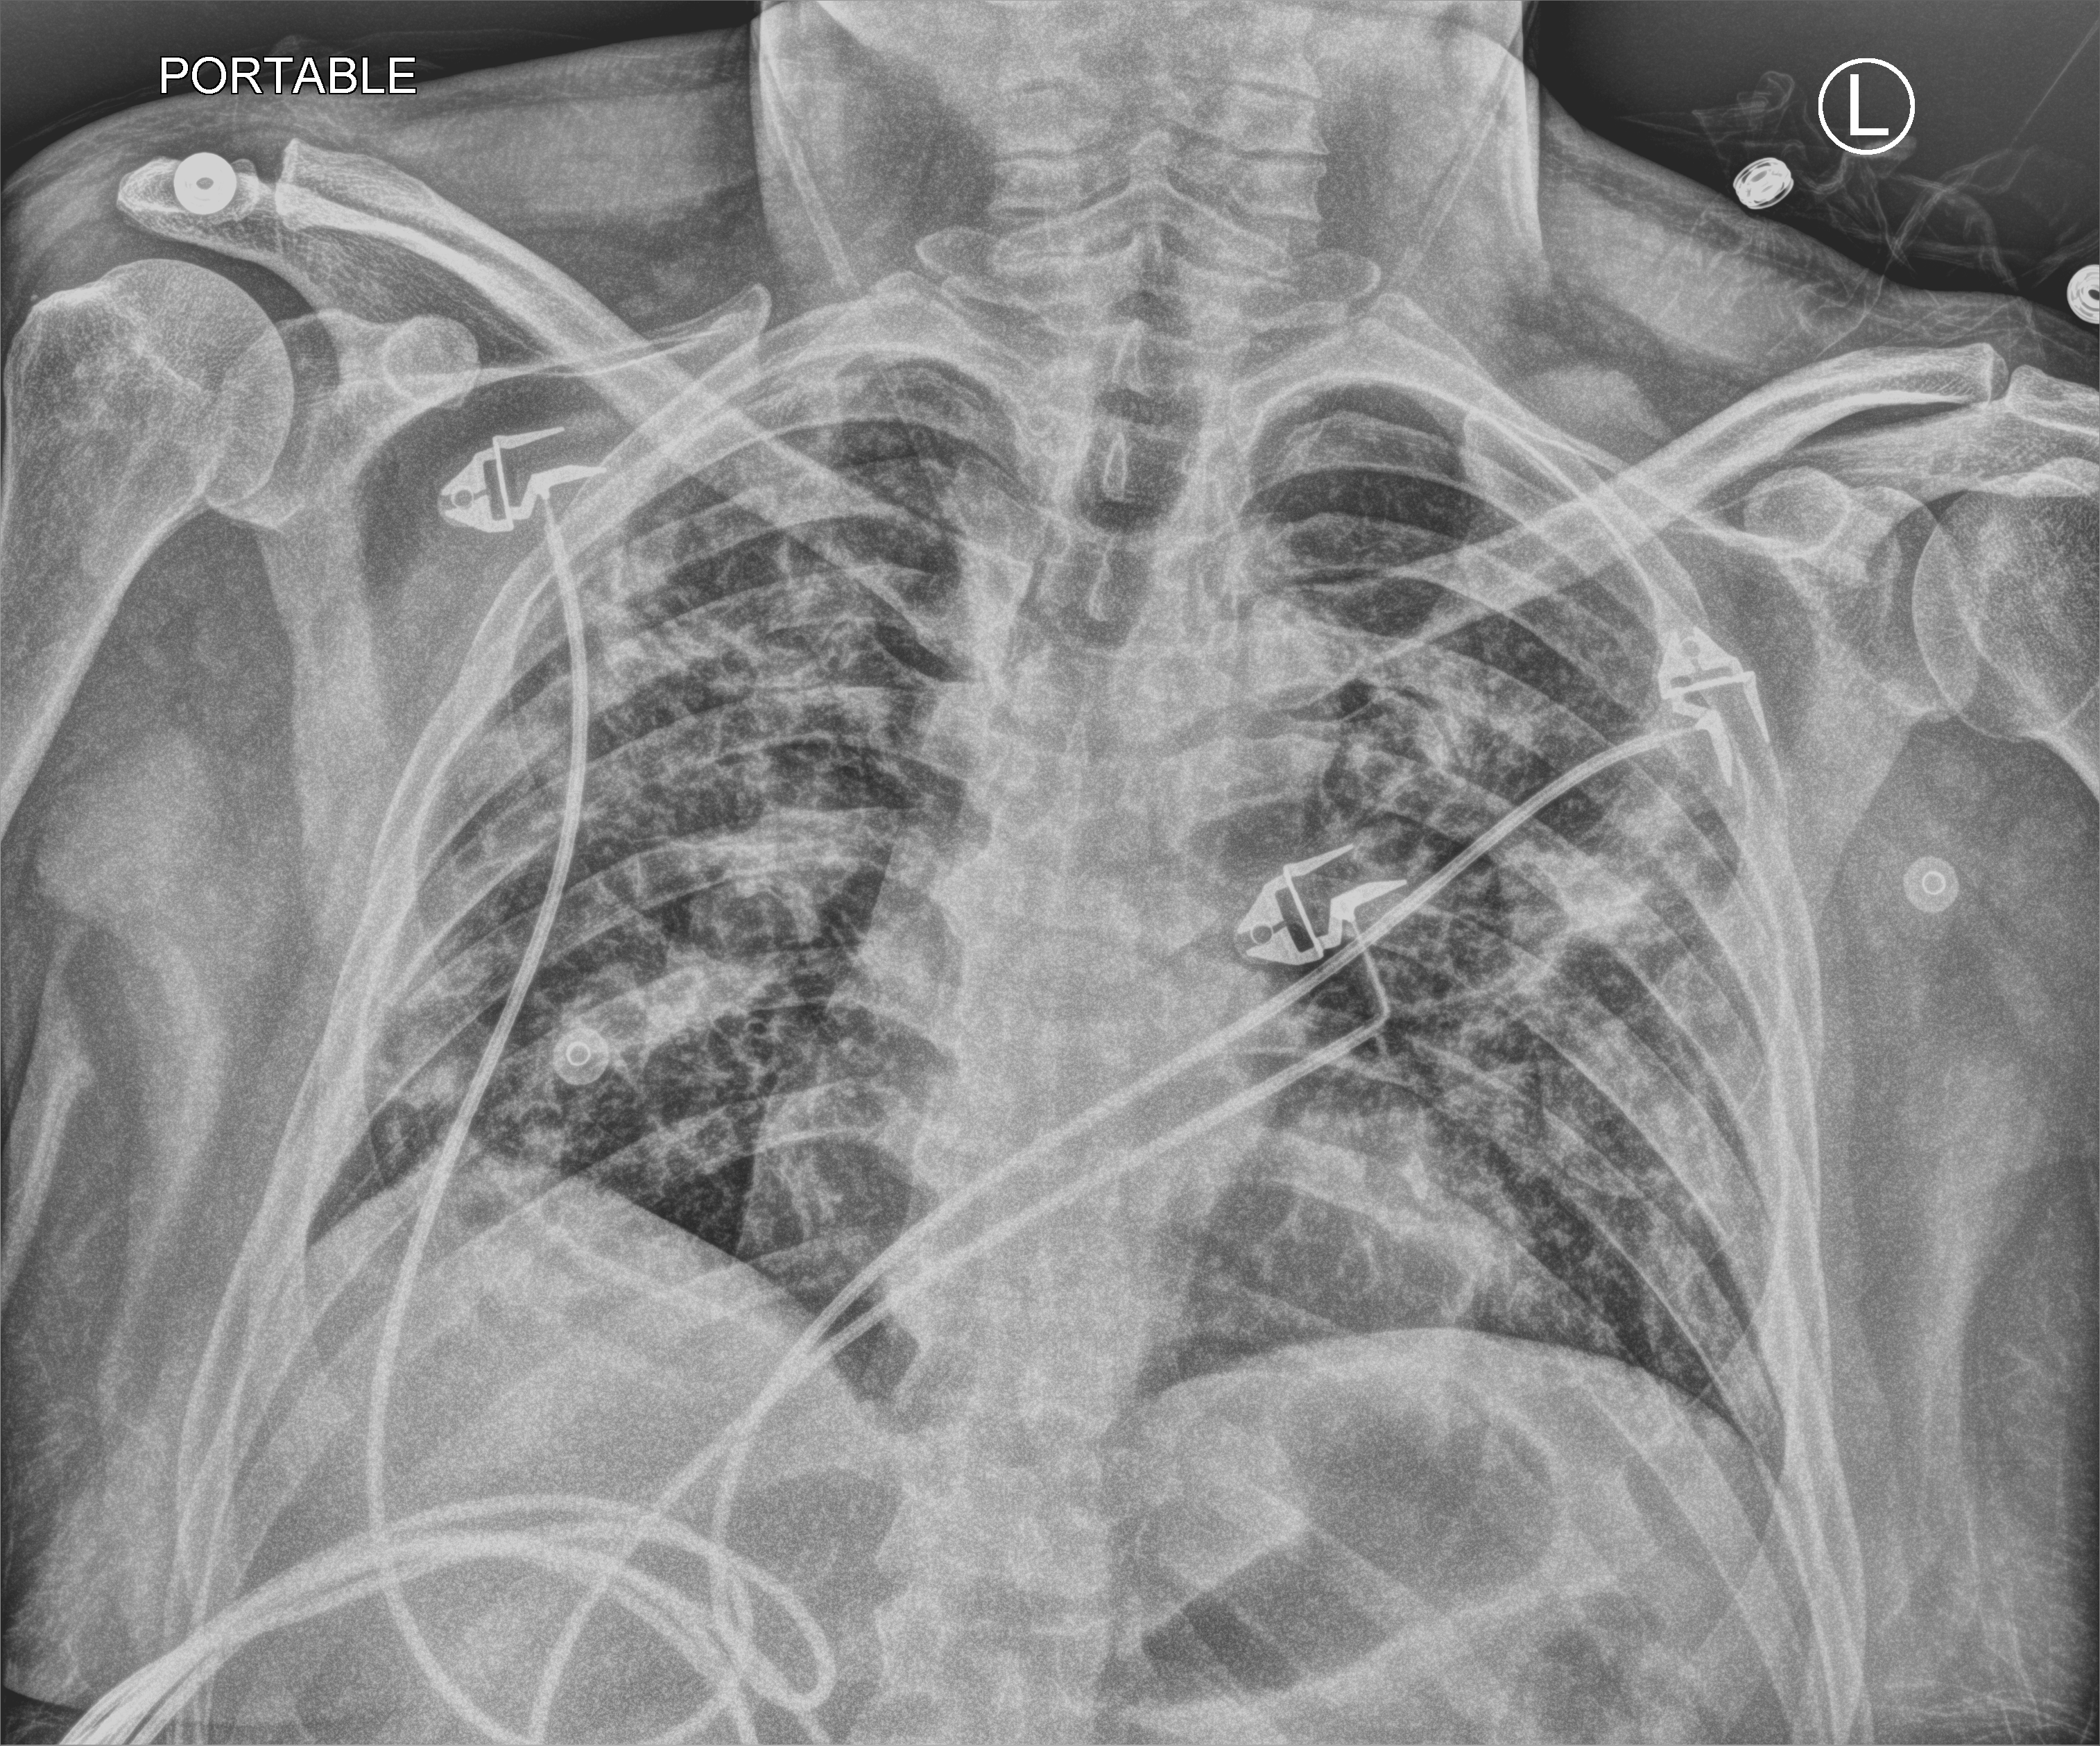
Chest X-ray (portable). Patient hospitalised with COVID-19; male, aged 18–59 years.
Hospital-stay facts (about this admission, not read from this image; timing relative to this image not recorded): mechanically ventilated during this hospital stay: no.